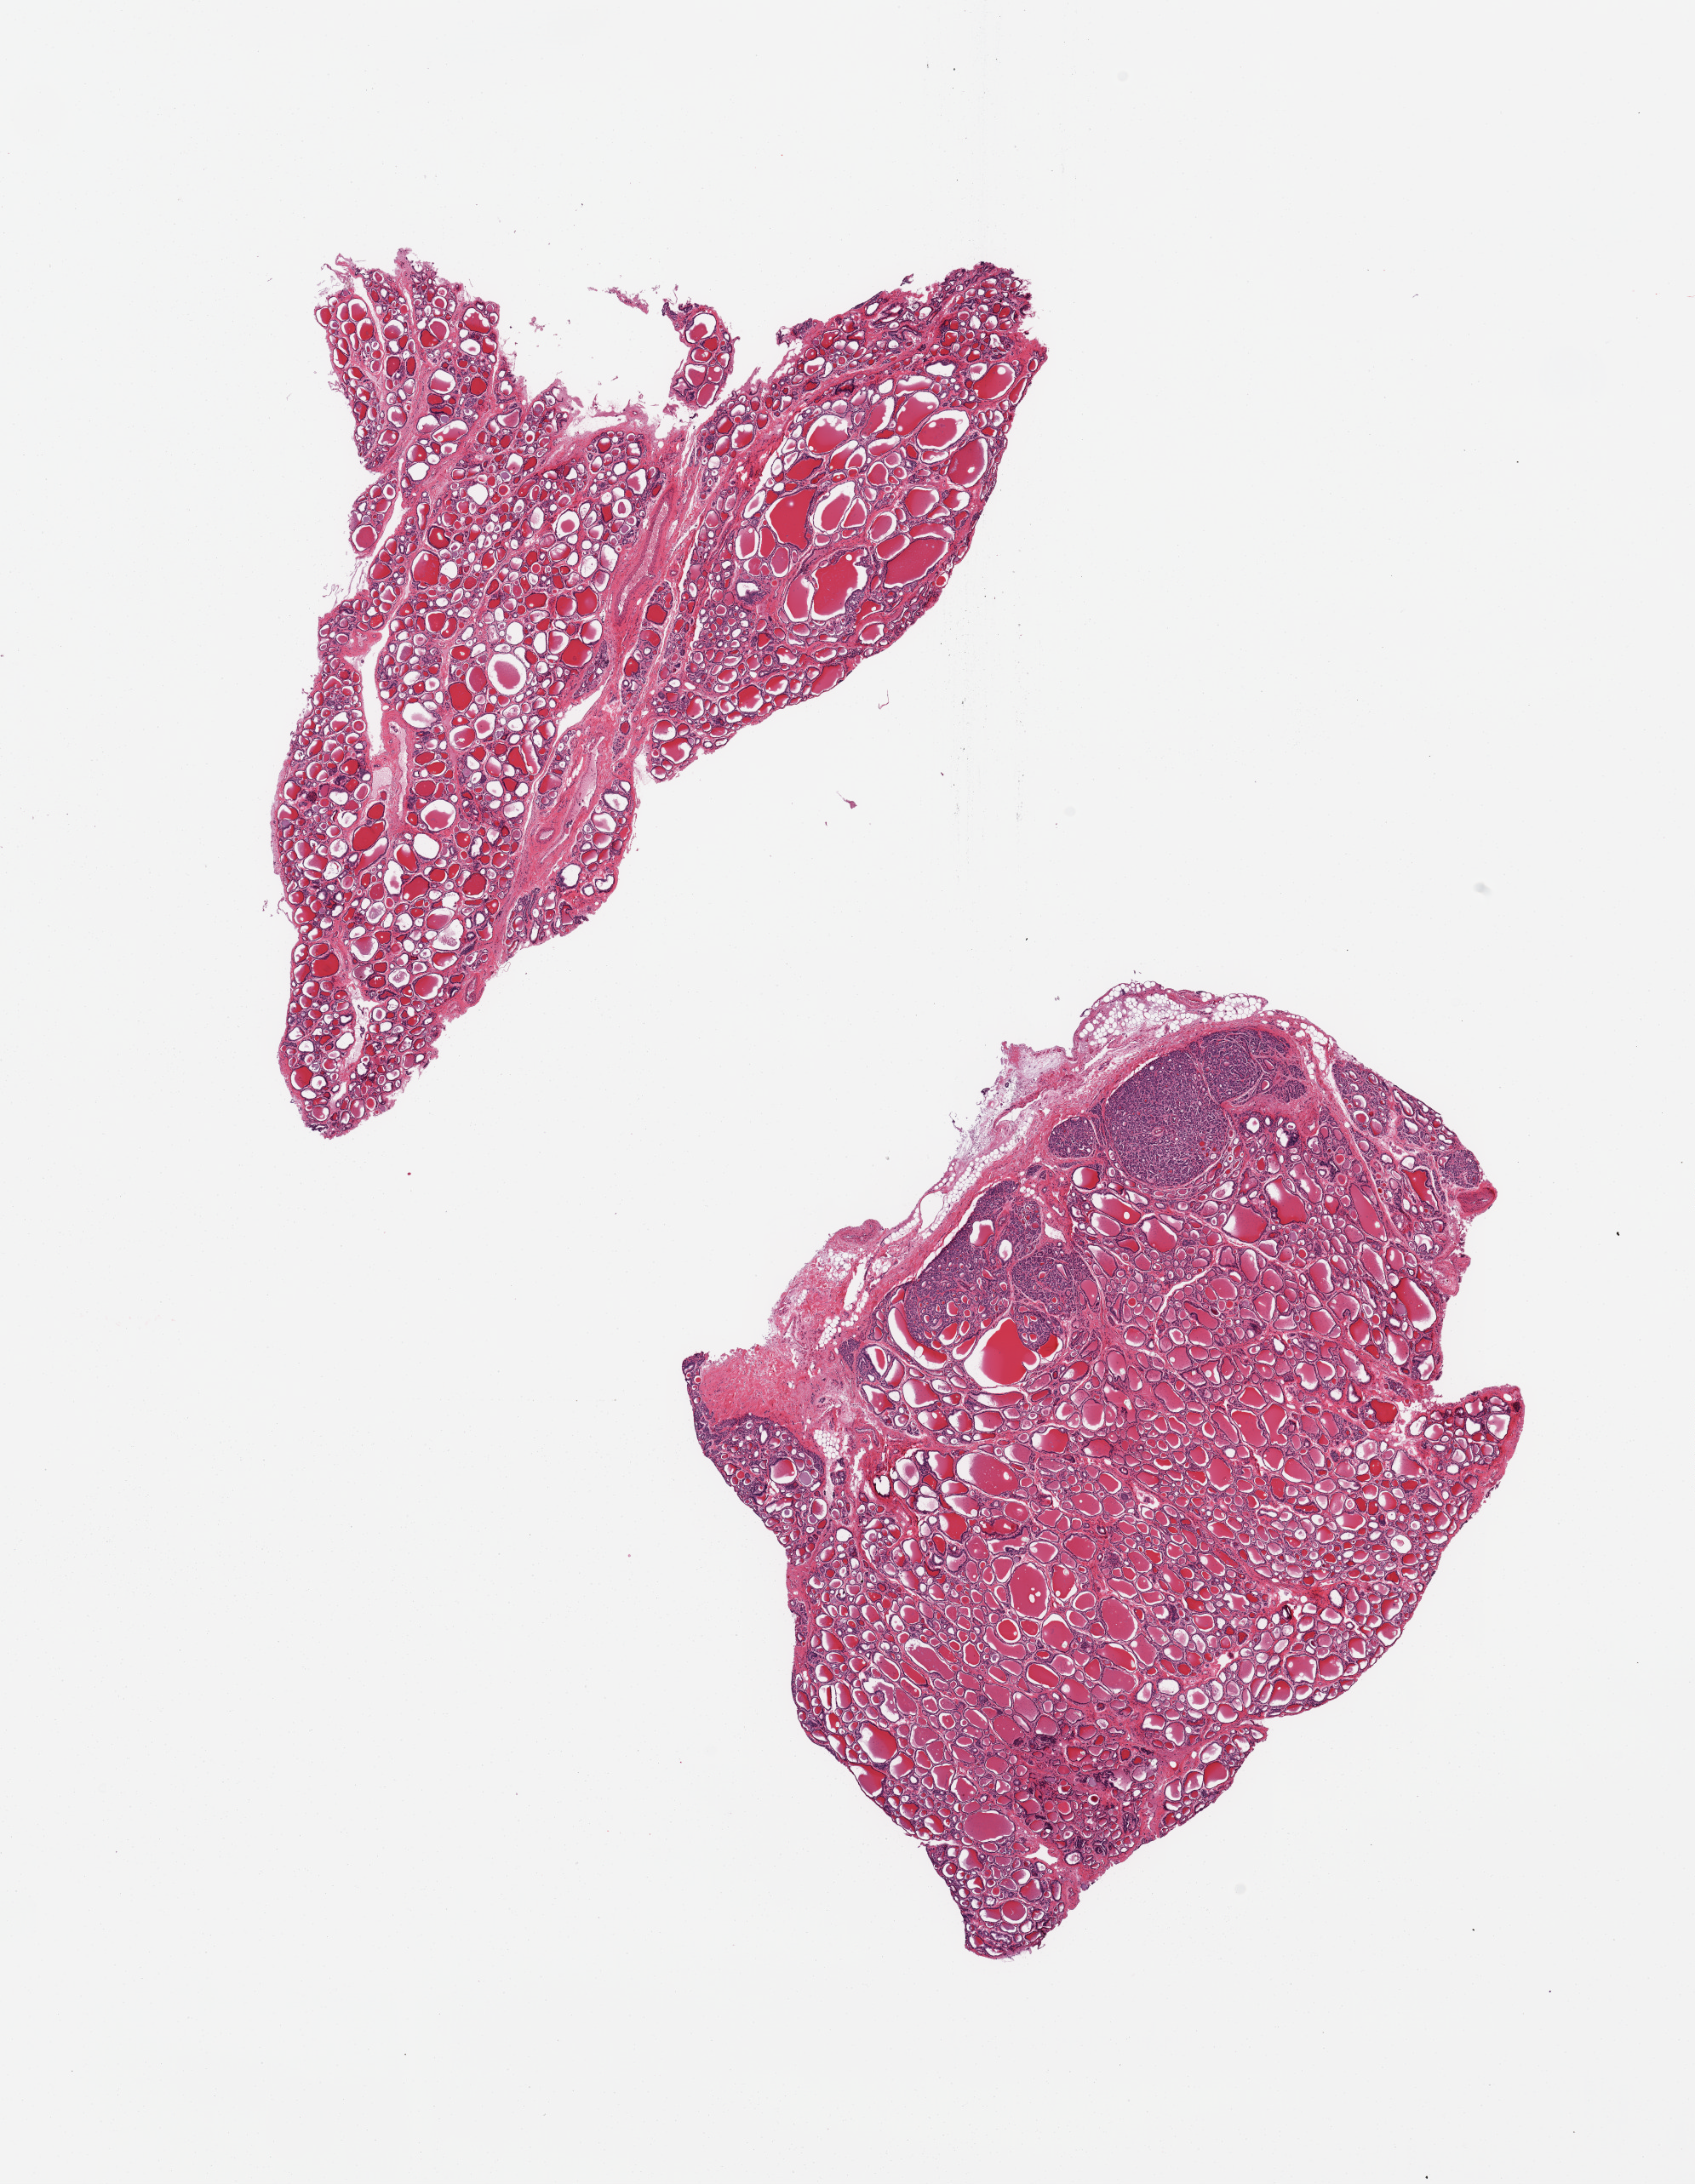
Digitized H&E-stained section — low-resolution overview of the scanned area, about 15.8 x 20.3 mm. PAXgene-fixed paraffin-embedded (PFPE) section. Sampled site (target tissue): thyroid. Donor tissue sample. Donor: male.
• pathologist's review note for this sample: 2 pieces; adenomatous nodular hyperplasia